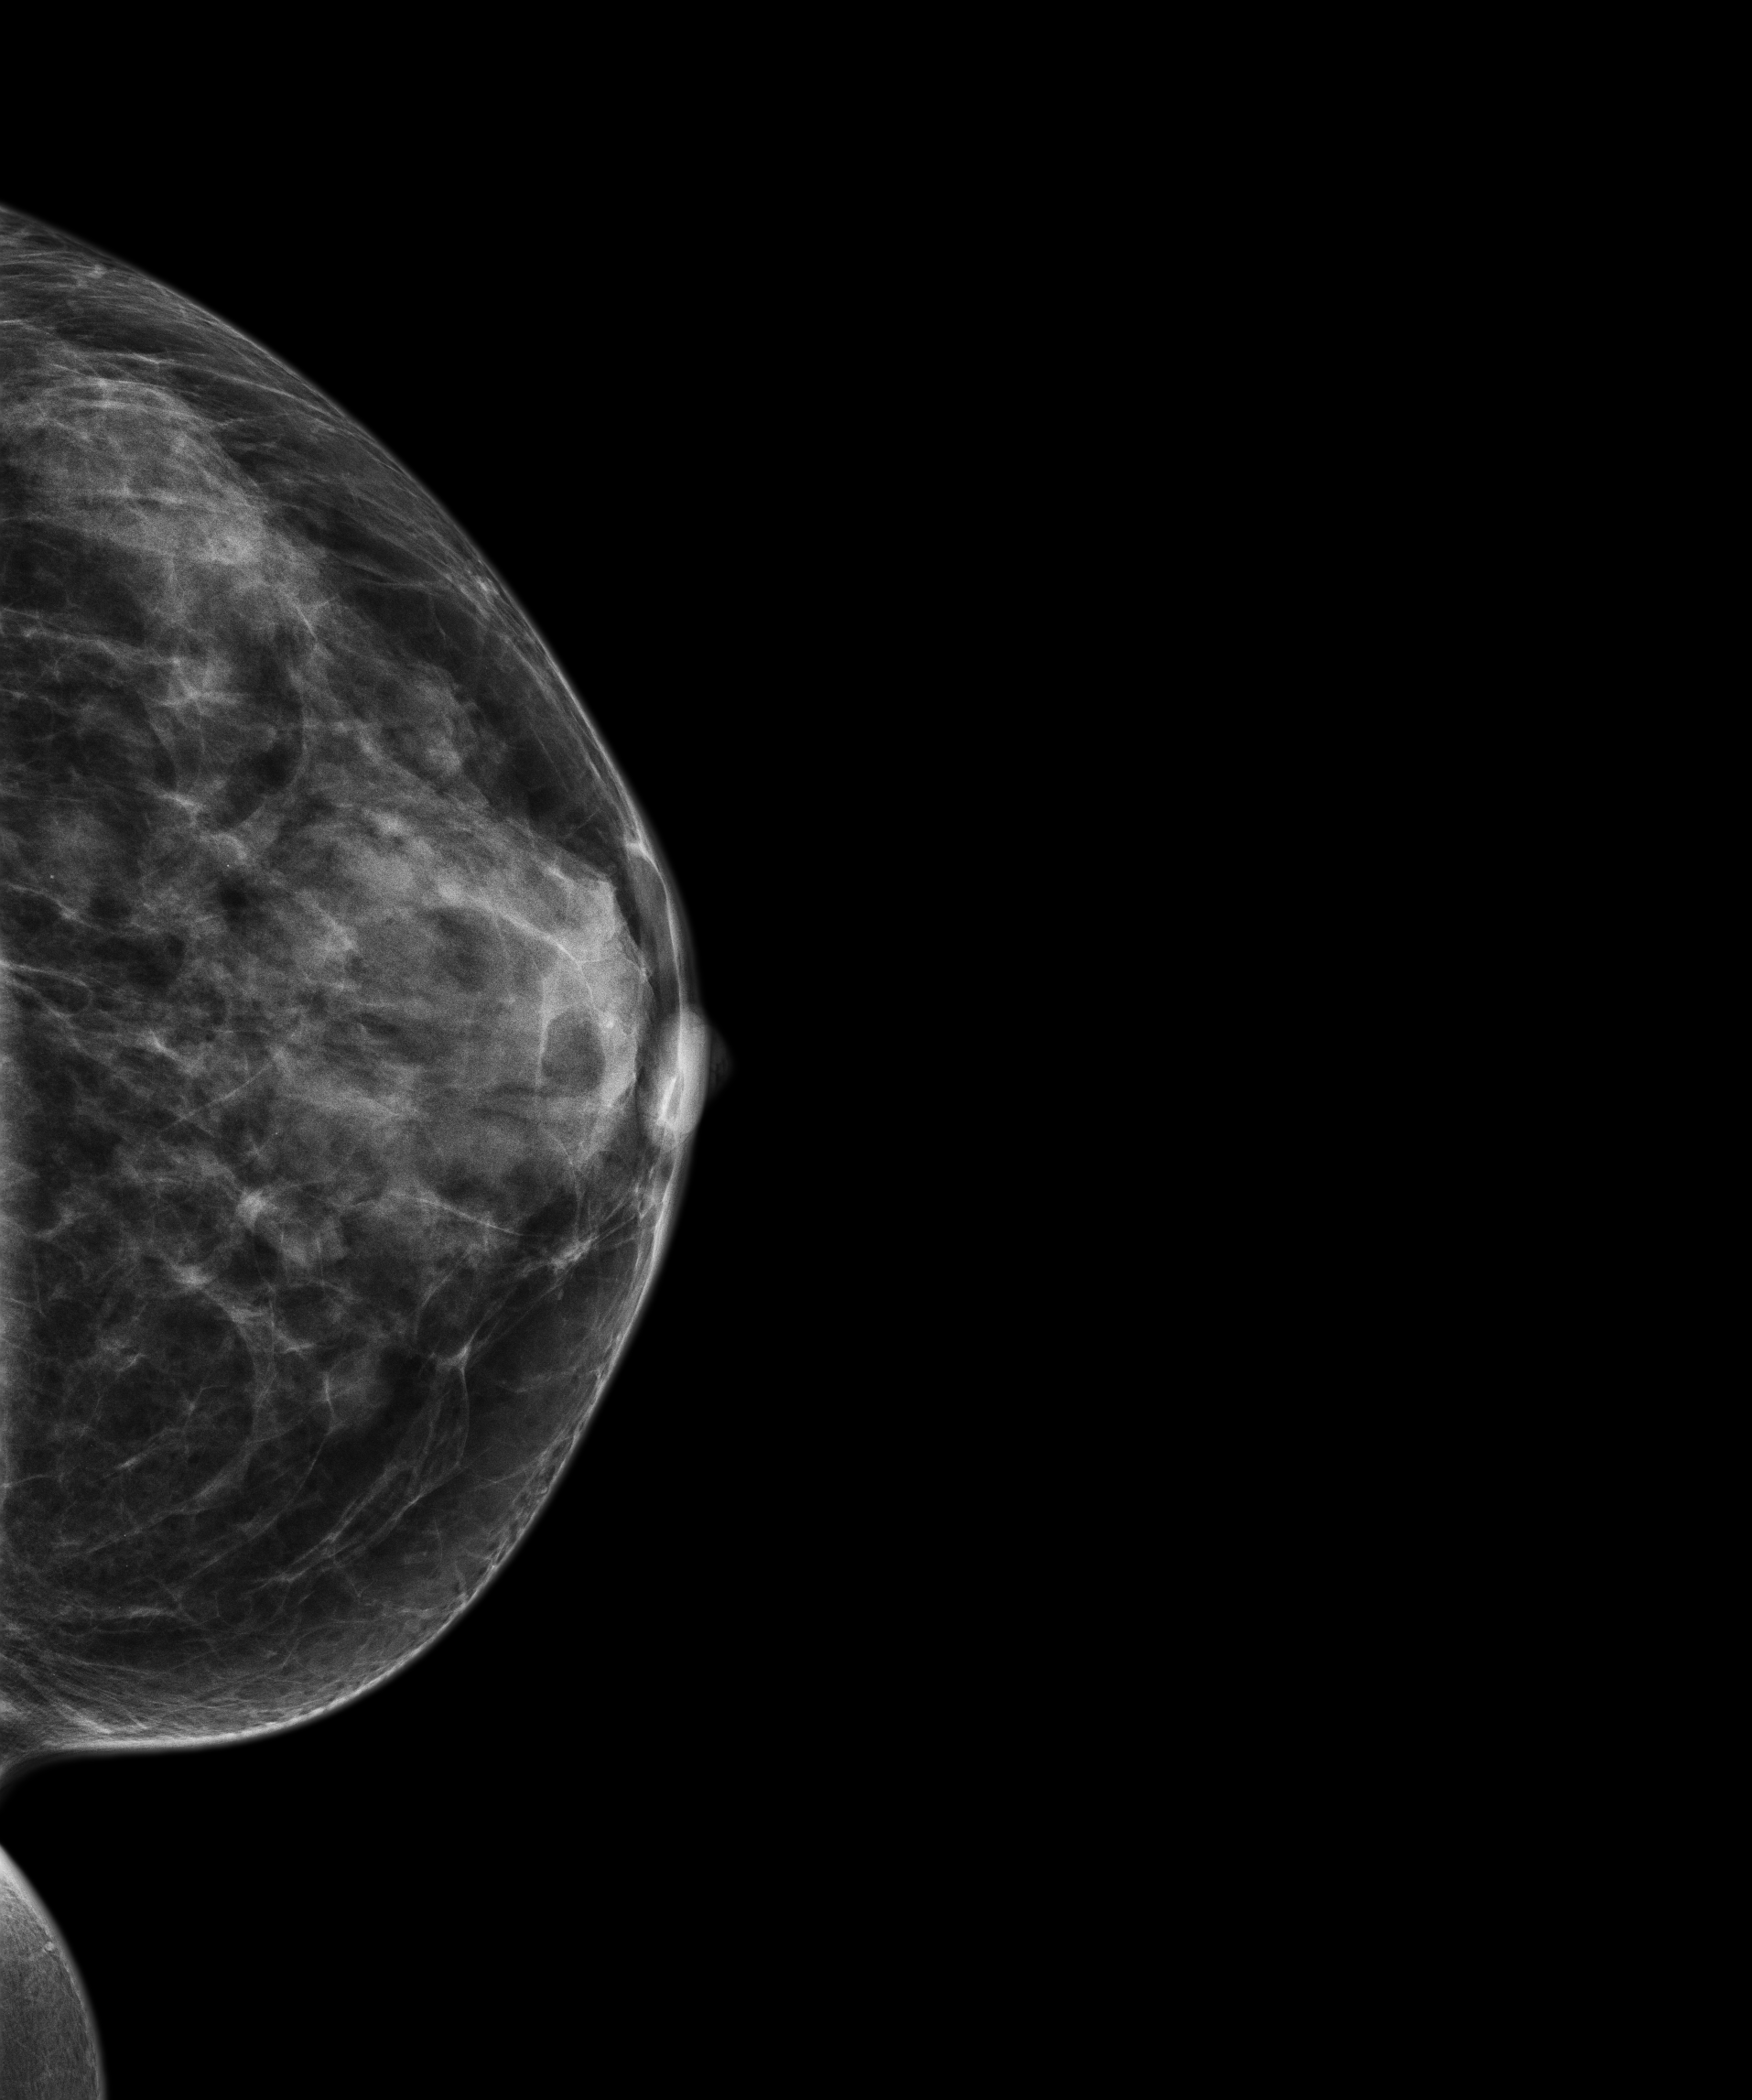
Screening examination. Patient aged 49 years (female).
Image type: full-field digital mammogram. Breast: left. Projection: CC view.